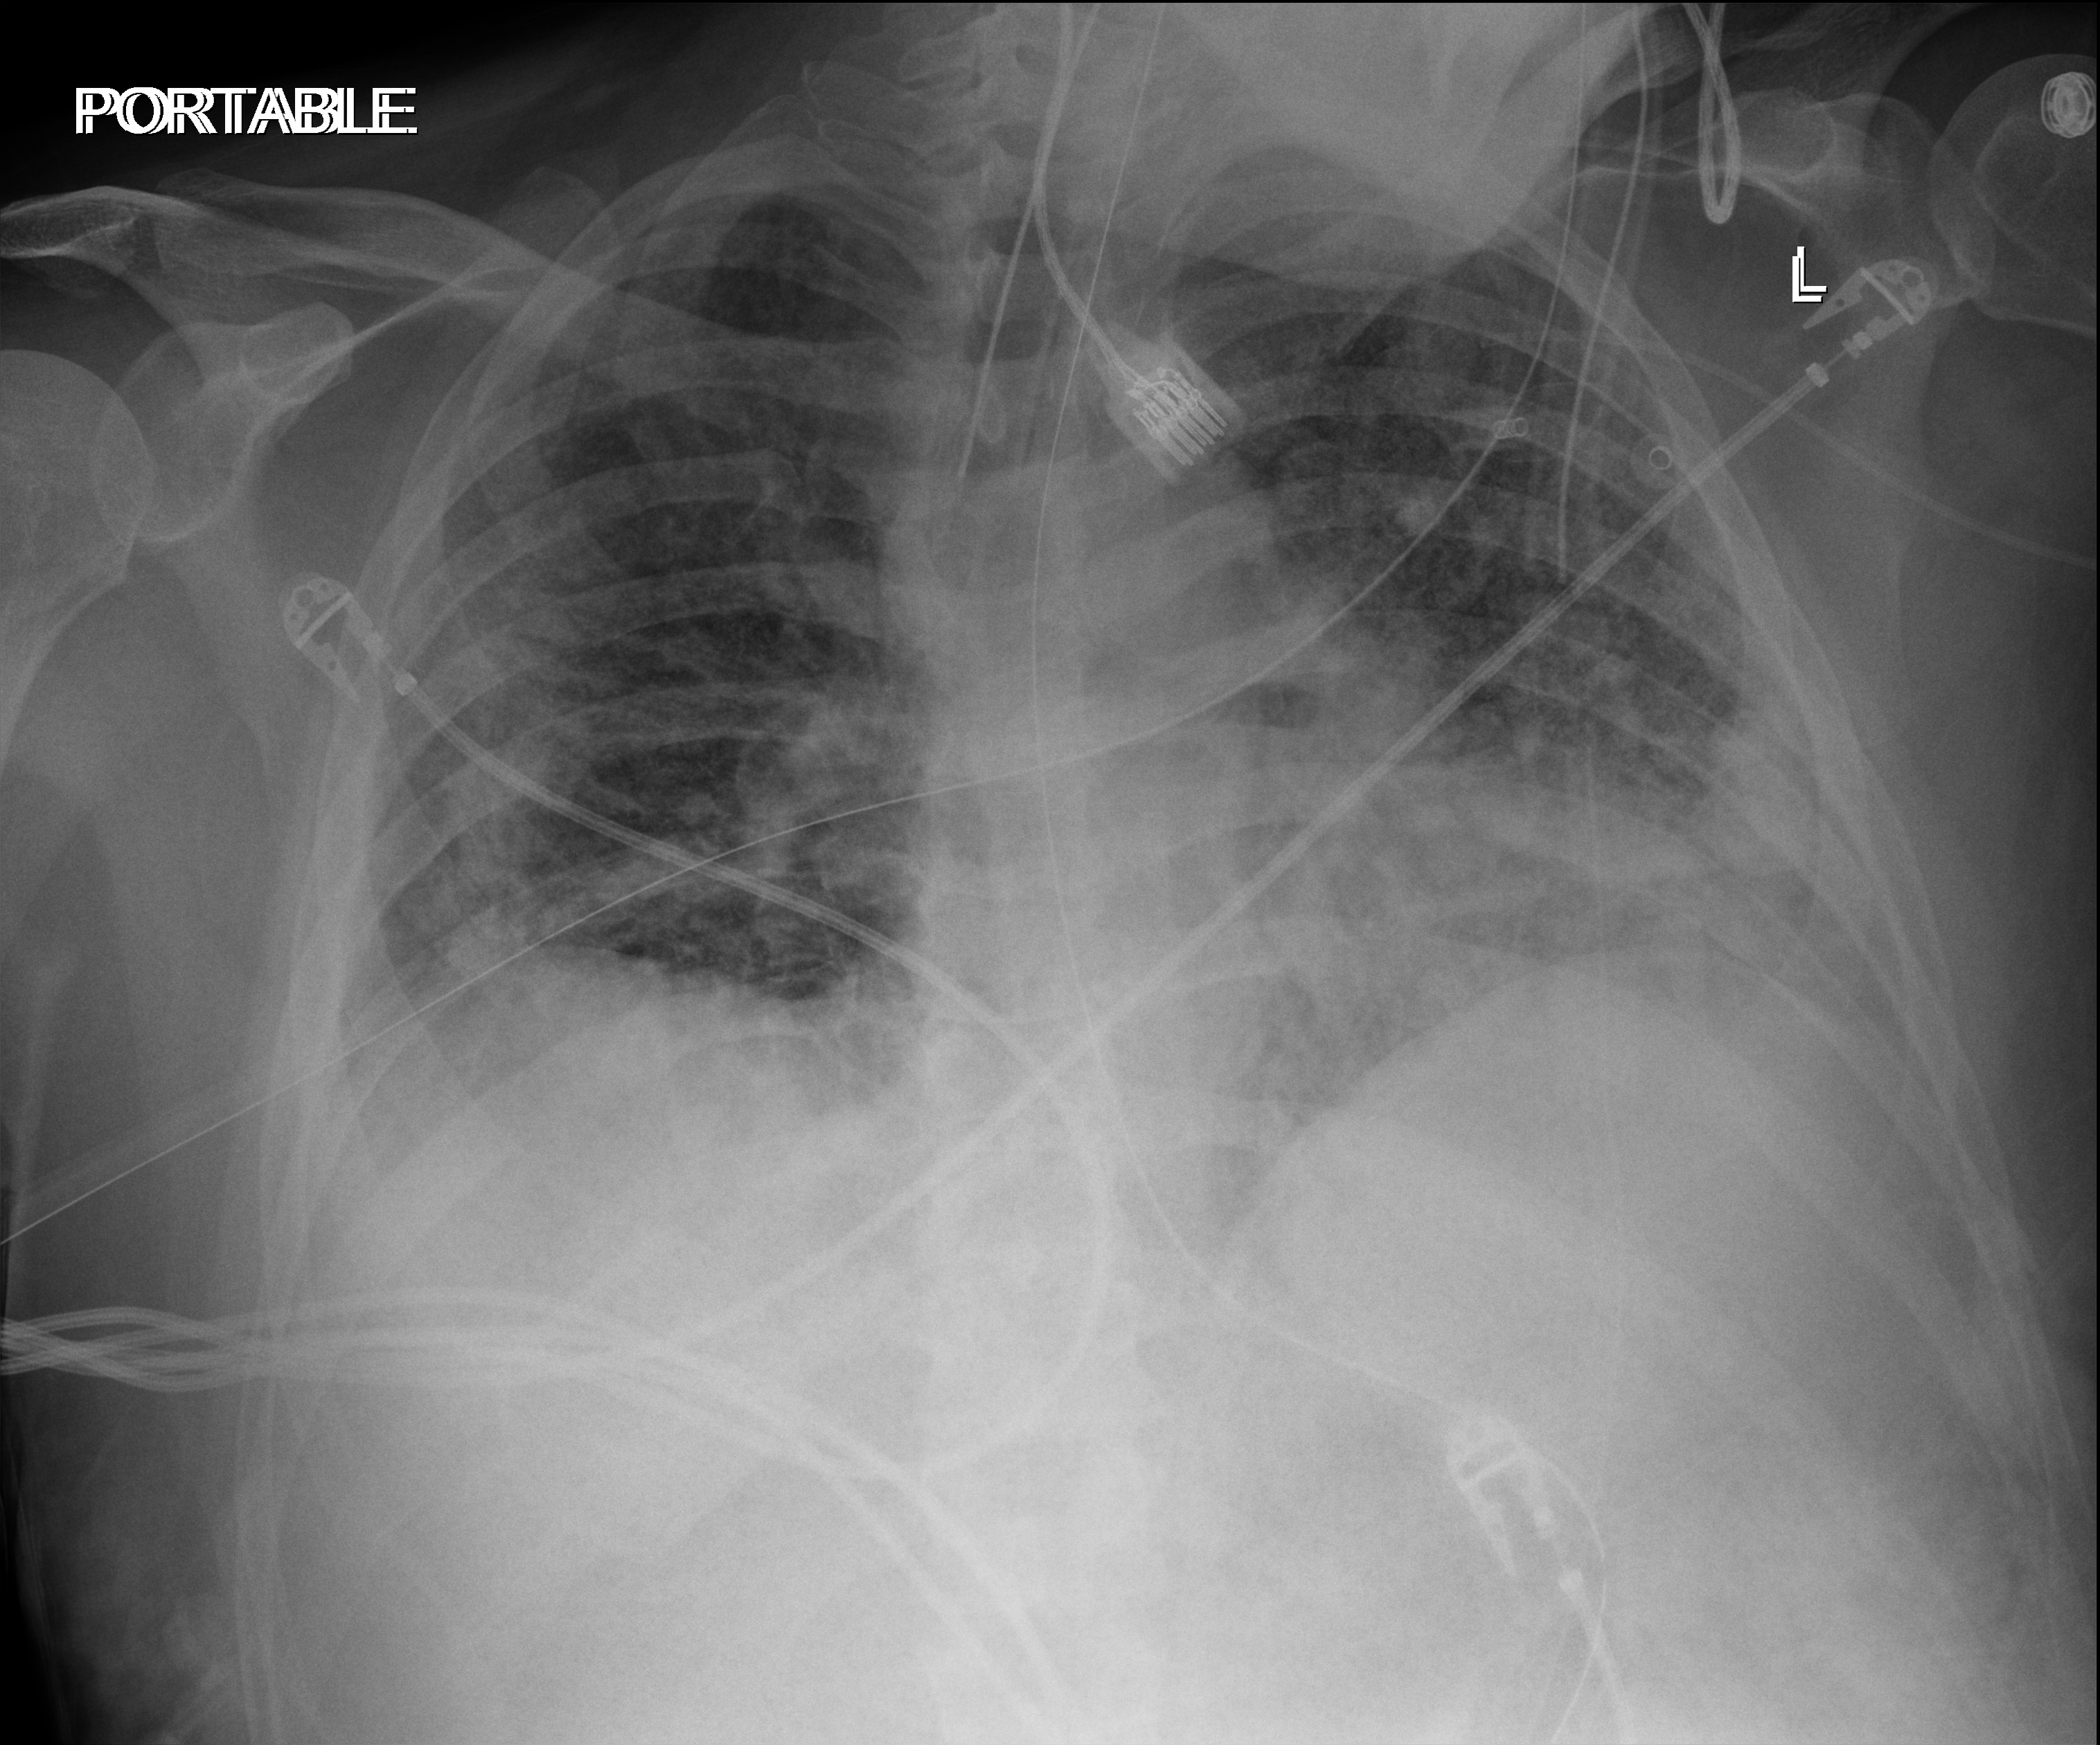
Chest radiograph (digital radiography). Patient hospitalised with COVID-19; male, aged 18–59 years.
Hospital-stay facts (about this admission, not read from this image; timing relative to this image not recorded): admitted to intensive care during this hospital stay: yes; smoking status (admission record): never; chronic kidney disease (admission record): no.